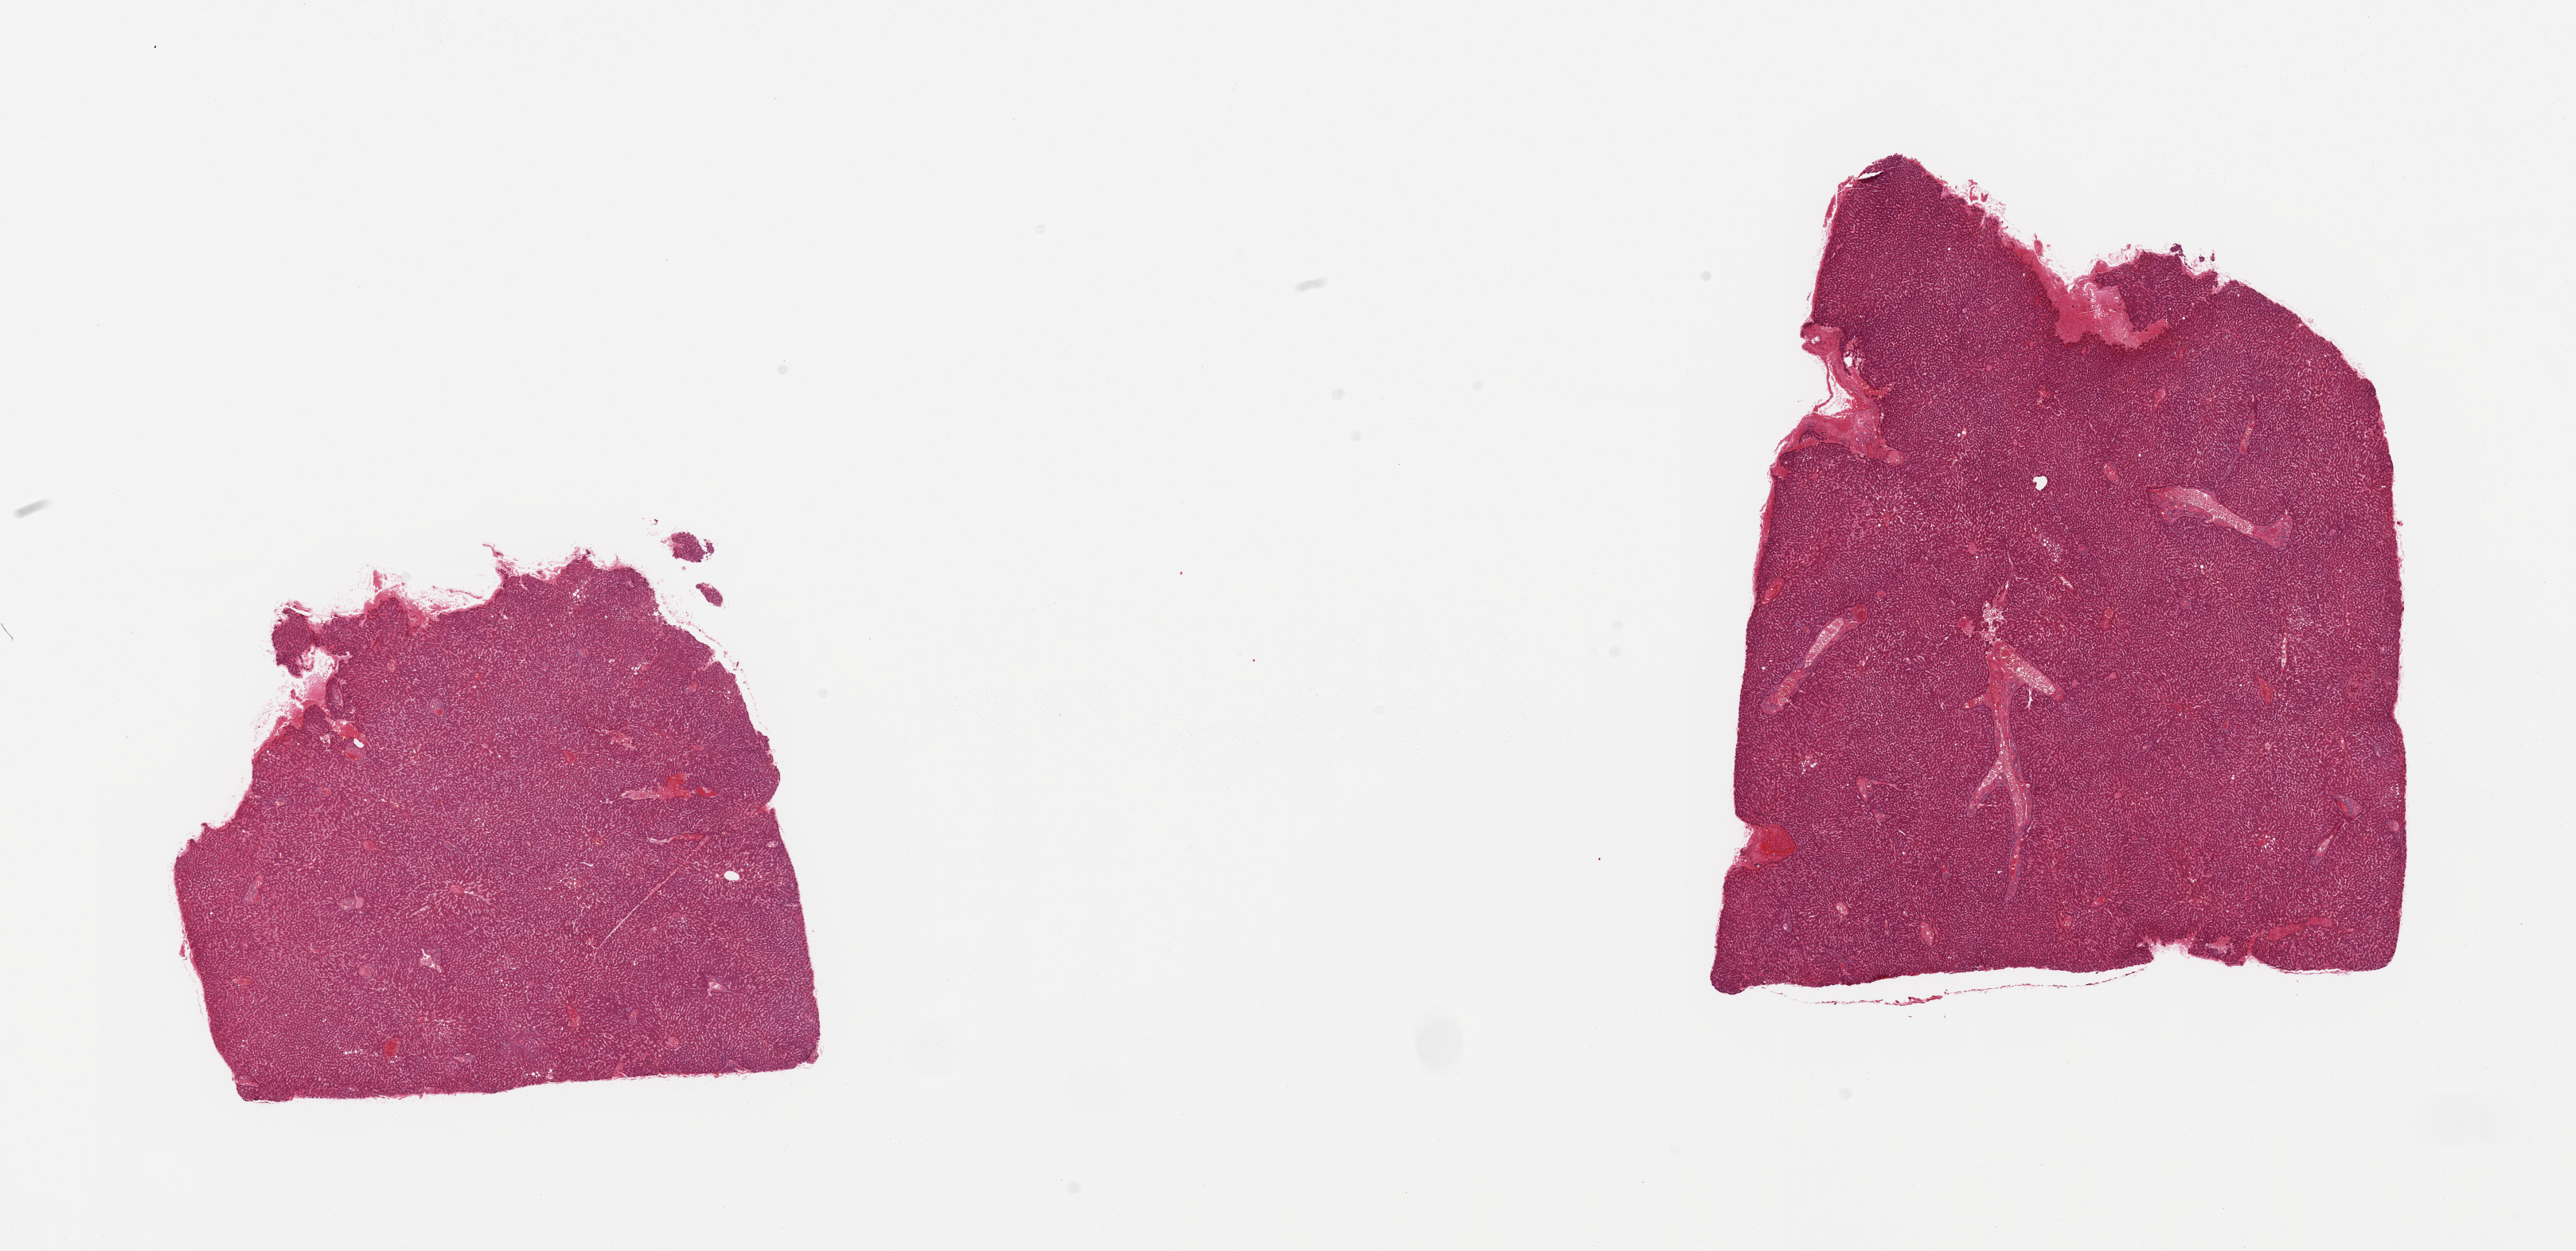
Whole-slide image, haematoxylin and eosin stain, brightfield — shown as a low-resolution overview of the whole scanned area (about 25.6 x 12.4 mm, slide scanned at 20x). PAXgene-fixed, paraffin-embedded tissue. Sampled site (target tissue): liver. Donor tissue sample. Donor: male.
* review note (as recorded): 2 pieces, minimal steatosis